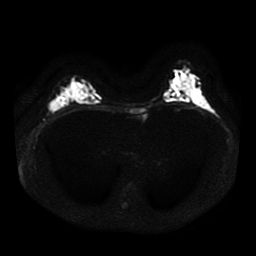
Breast MRI, one axial slice. Position 25 of 41 along the scan axis. Diffusion-weighted series; image 2 of 4 stored at this slice position (different b-values; order by instance number). 1.5 T. 5 mm slice thickness. 256 × 256 image matrix, field of view 330 × 330 mm. Female patient.
Outlined on this slice (outlined manually by an expert reader):
- tumour on diffusion-weighted imaging: box from (x=50, y=100) to (x=60, y=110) px